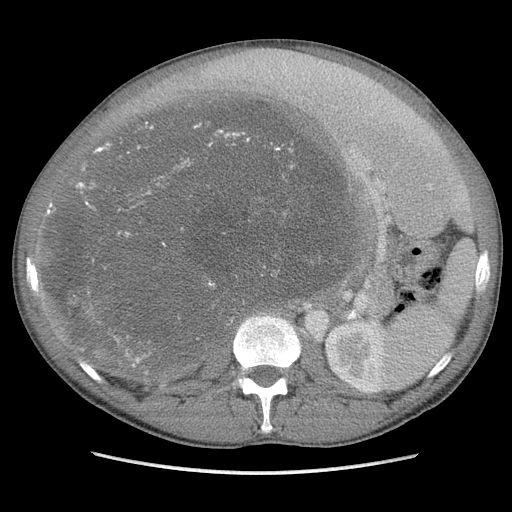
Contrast-enhanced abdominal CT, one axial slice; soft-tissue window (W 400 / L 40 HU); 5 mm slice thickness; 512 × 512 image matrix. Male patient. From the clinical record (not read from this slice): diagnosis: adrenocortical carcinoma; tumour side: right adrenal; Ki-67 index: 13 %; stage (as recorded): 3.
Structures marked on this image (semi-automatically segmented with operator editing):
- mass: bounding box (x1, y1, x2, y2) in pixels: (54, 93, 367, 365)